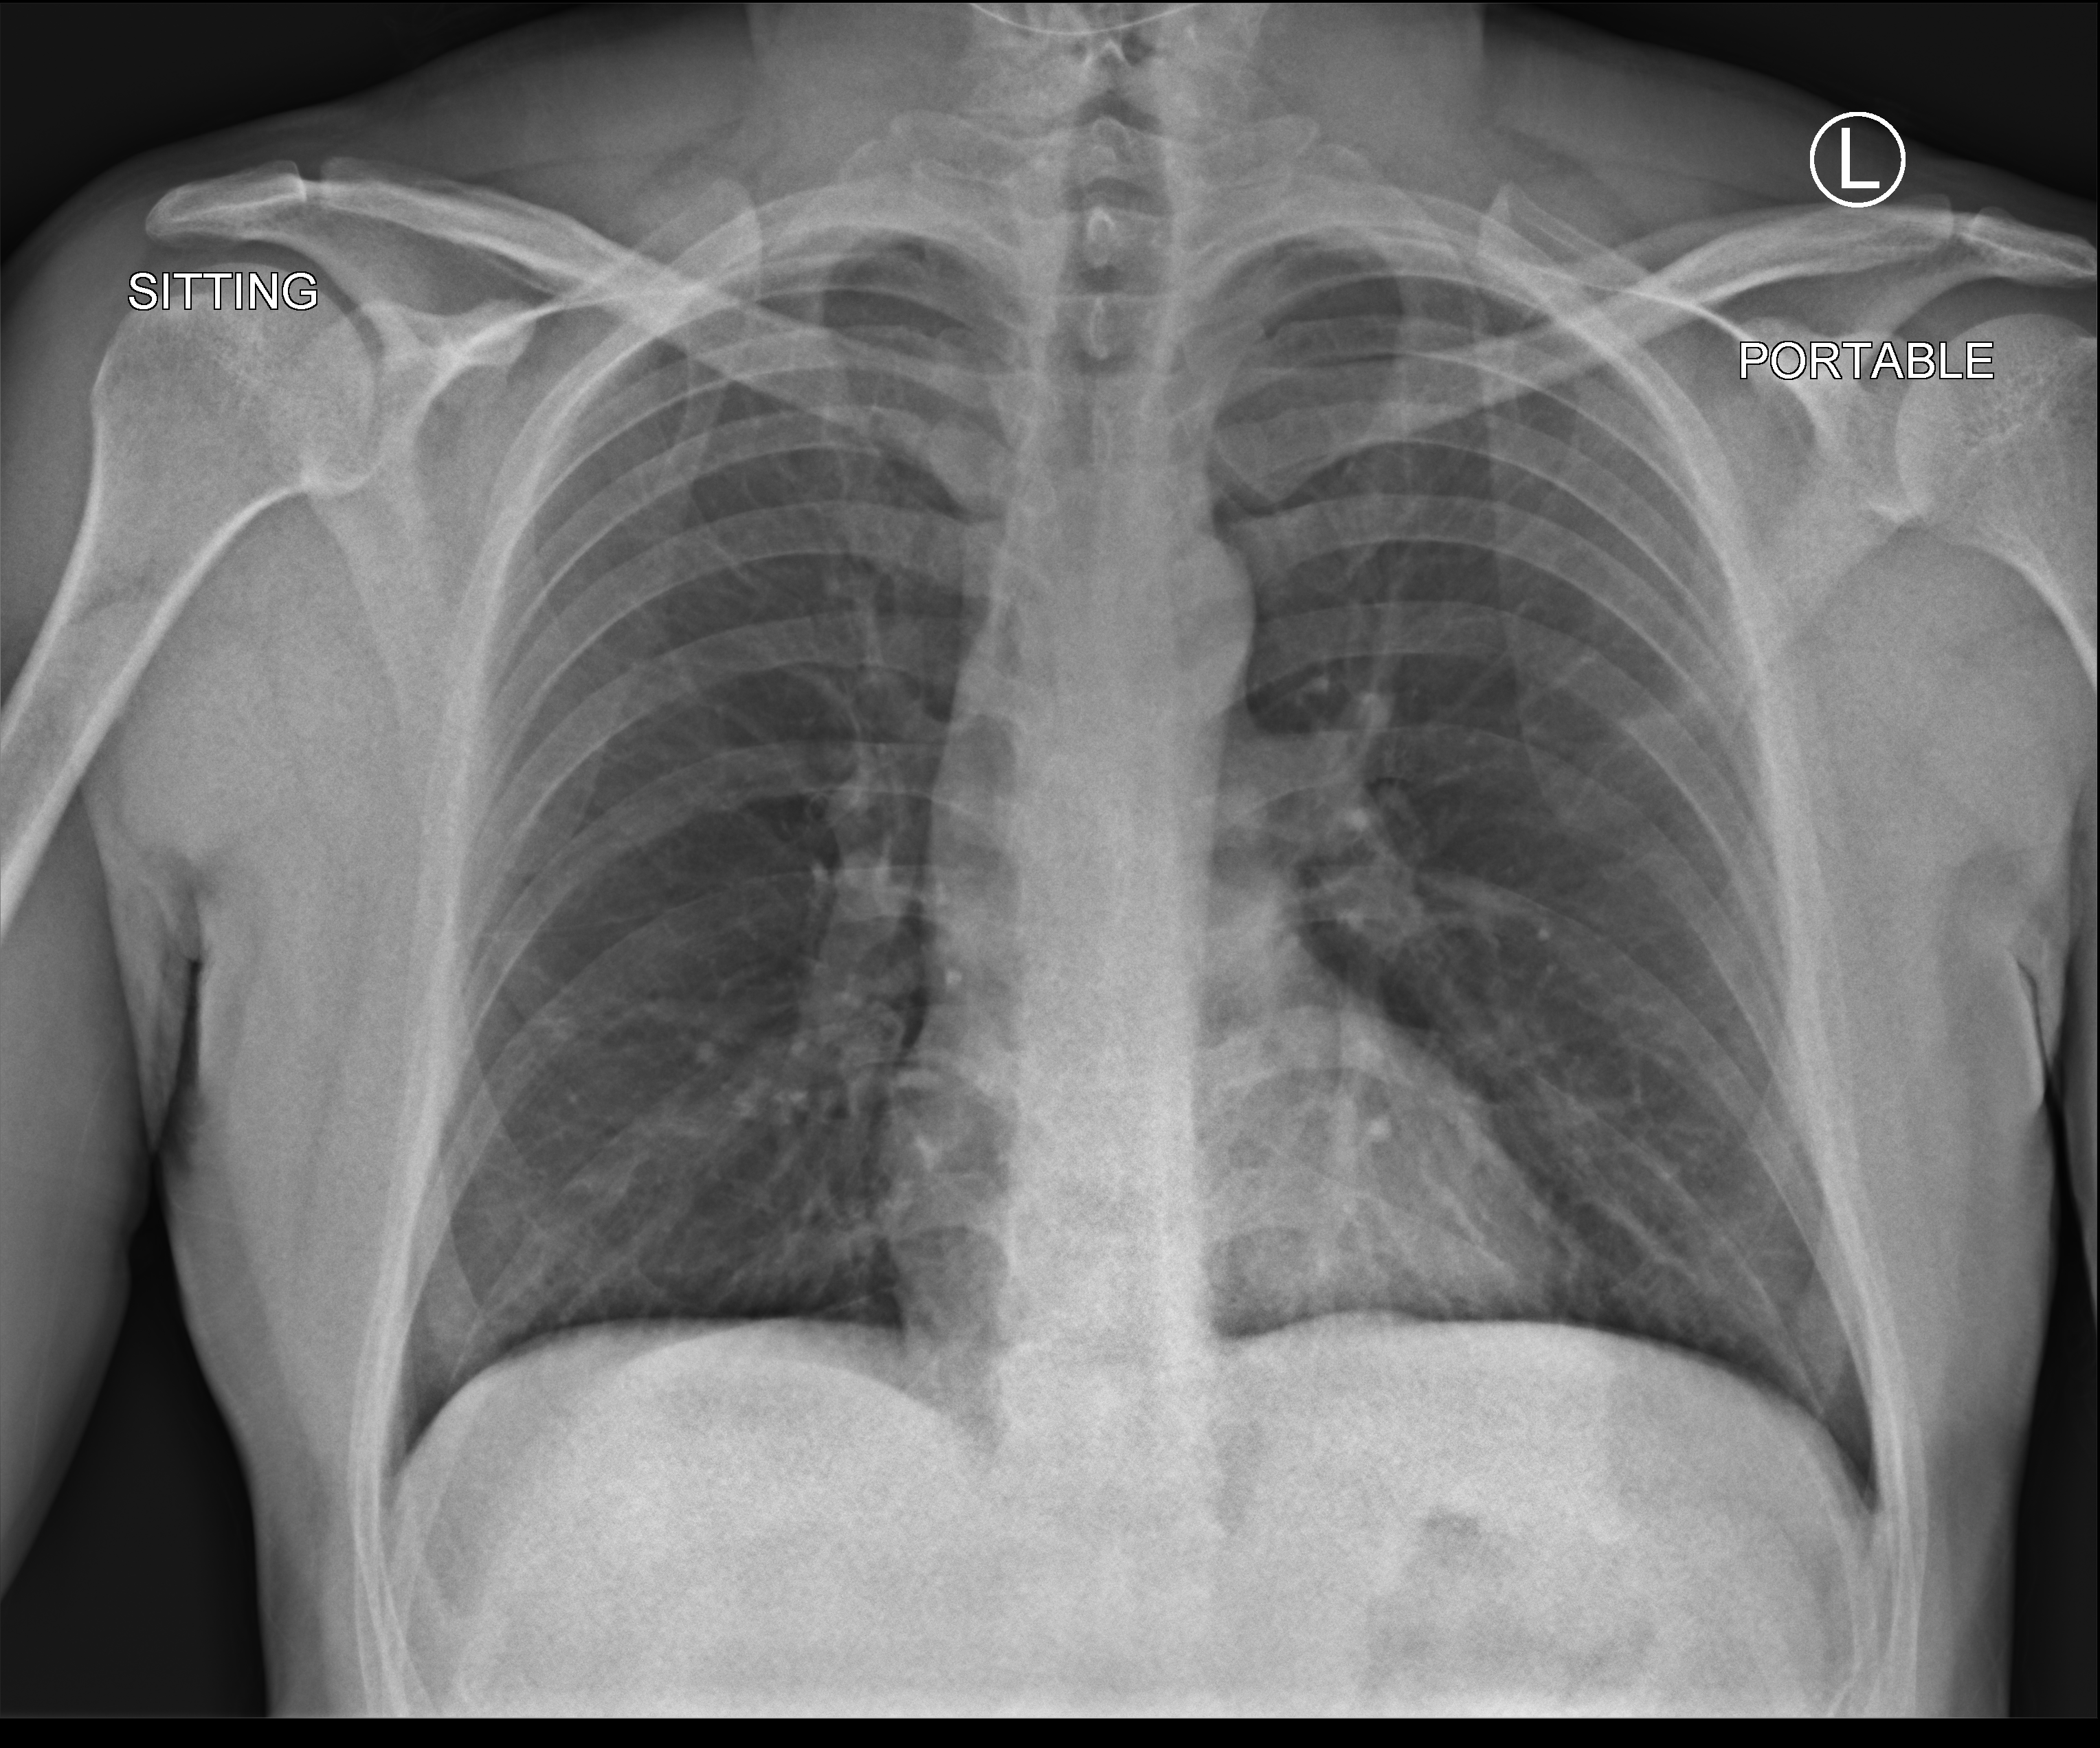
Chest X-ray (portable); anteroposterior (AP) projection. Male patient hospitalised with COVID-19, age 18–59 years.
Hospital-stay facts (about this admission, not read from this image; timing relative to this image not recorded): COPD (admission record): no; mechanically ventilated during this hospital stay: no.